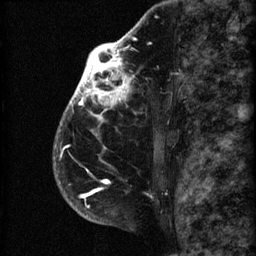
Breast MRI (dynamic contrast-enhanced), one sagittal slice. Position 47 of 60 along the scan axis. 3 images stored at this slice position (order not interpretable as contrast timing). 1.5 T. TE 4.2 ms, TR 22.7 ms. 2 mm slice thickness. 256 × 256 image matrix, field of view 180 × 180 mm. Female patient, age 48 years. From the clinical record (not read from this slice): setting: breast cancer imaged before/during neoadjuvant chemotherapy; receptor status: triple-negative.
Structures marked on this image (semi-automatically segmented with operator editing):
- analysis volume of interest (the breast-tissue region the enhancement analysis was run in; not a lesion): box from (x=53, y=30) to (x=173, y=207) px
- tumour enhancement mask (voxels above the 90 % enhancement threshold inside the analysis volume of interest): (x=53, y=30)–(x=136, y=207)